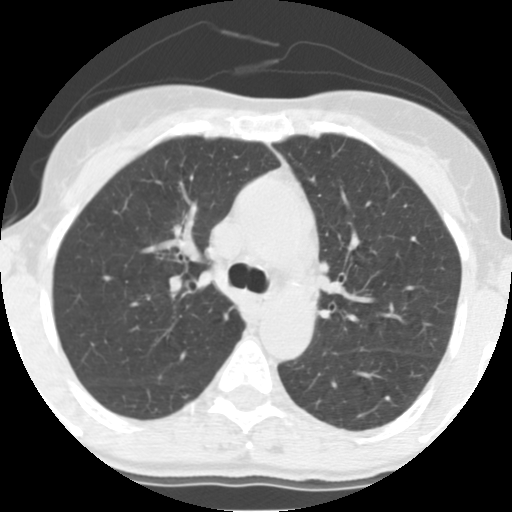
Axial slice from a low-dose chest CT screening exam, third screening round (two years after baseline), lung window (W 1500 / L -600 HU), 2.5 mm slice thickness, 140 kVp, slice 46 of 140 in the series, 512 × 512 image matrix. Female, age 56 years at enrolment. Former smoker at enrolment.
- Expert-annotated lung lesion, bounding box [x1, y1, x2, y2] px = [161, 210, 198, 245].
- Reader record for this screening exam (exam-level; its link to the box is not recorded): non-calcified nodule or mass ≥4 mm, right upper lobe, 17 × 12 mm, spiculated (stellate) margins, soft tissue attenuation, pre-existing on the prior screen: yes; interval growth: yes.
- Official screen result: positive, other.
- Participant outcome: lung cancer diagnosed 49 days after this screen — adenocarcinoma, NOS, right upper lobe, moderately differentiated (G2), stage IA (AJCC 6th edition), 19 mm at pathology.